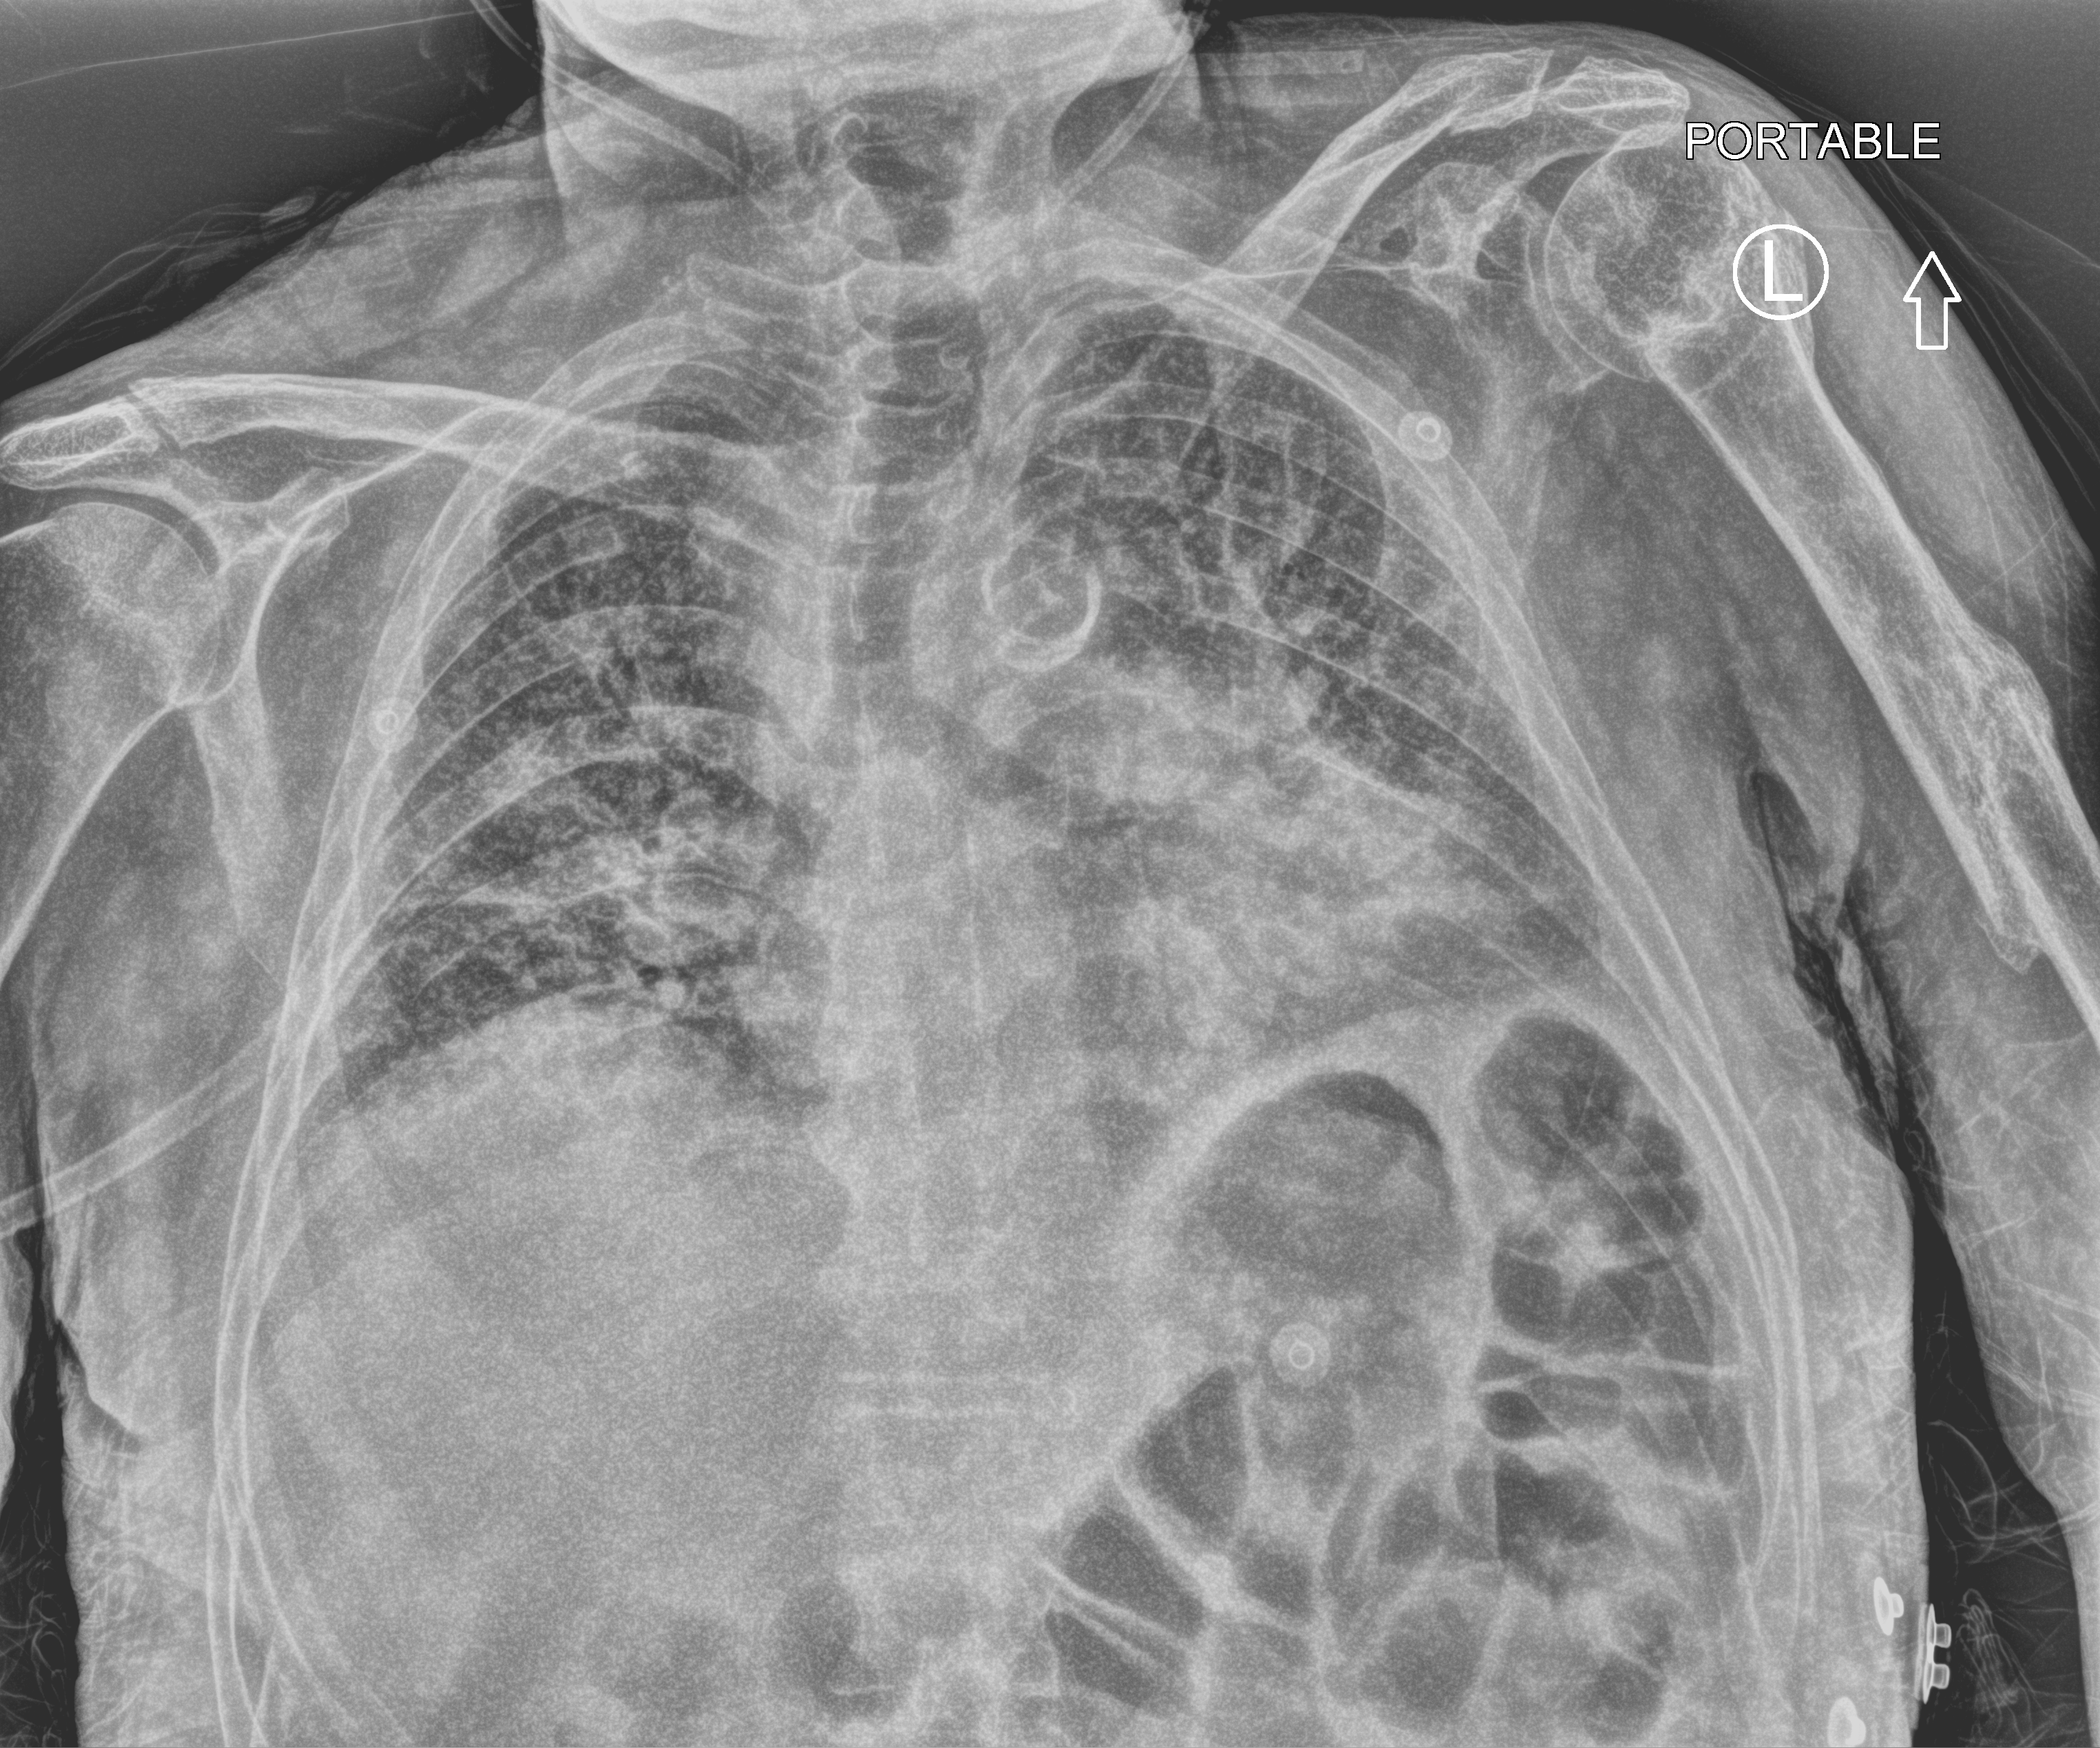
Chest X-ray (portable); anteroposterior (AP) projection. Male patient hospitalised with COVID-19, age 60–74 years.
Admission-level facts for this patient (not findings on this image; timing relative to this image not recorded): hypertension (admission record): yes; admitted to intensive care during this hospital stay: no.